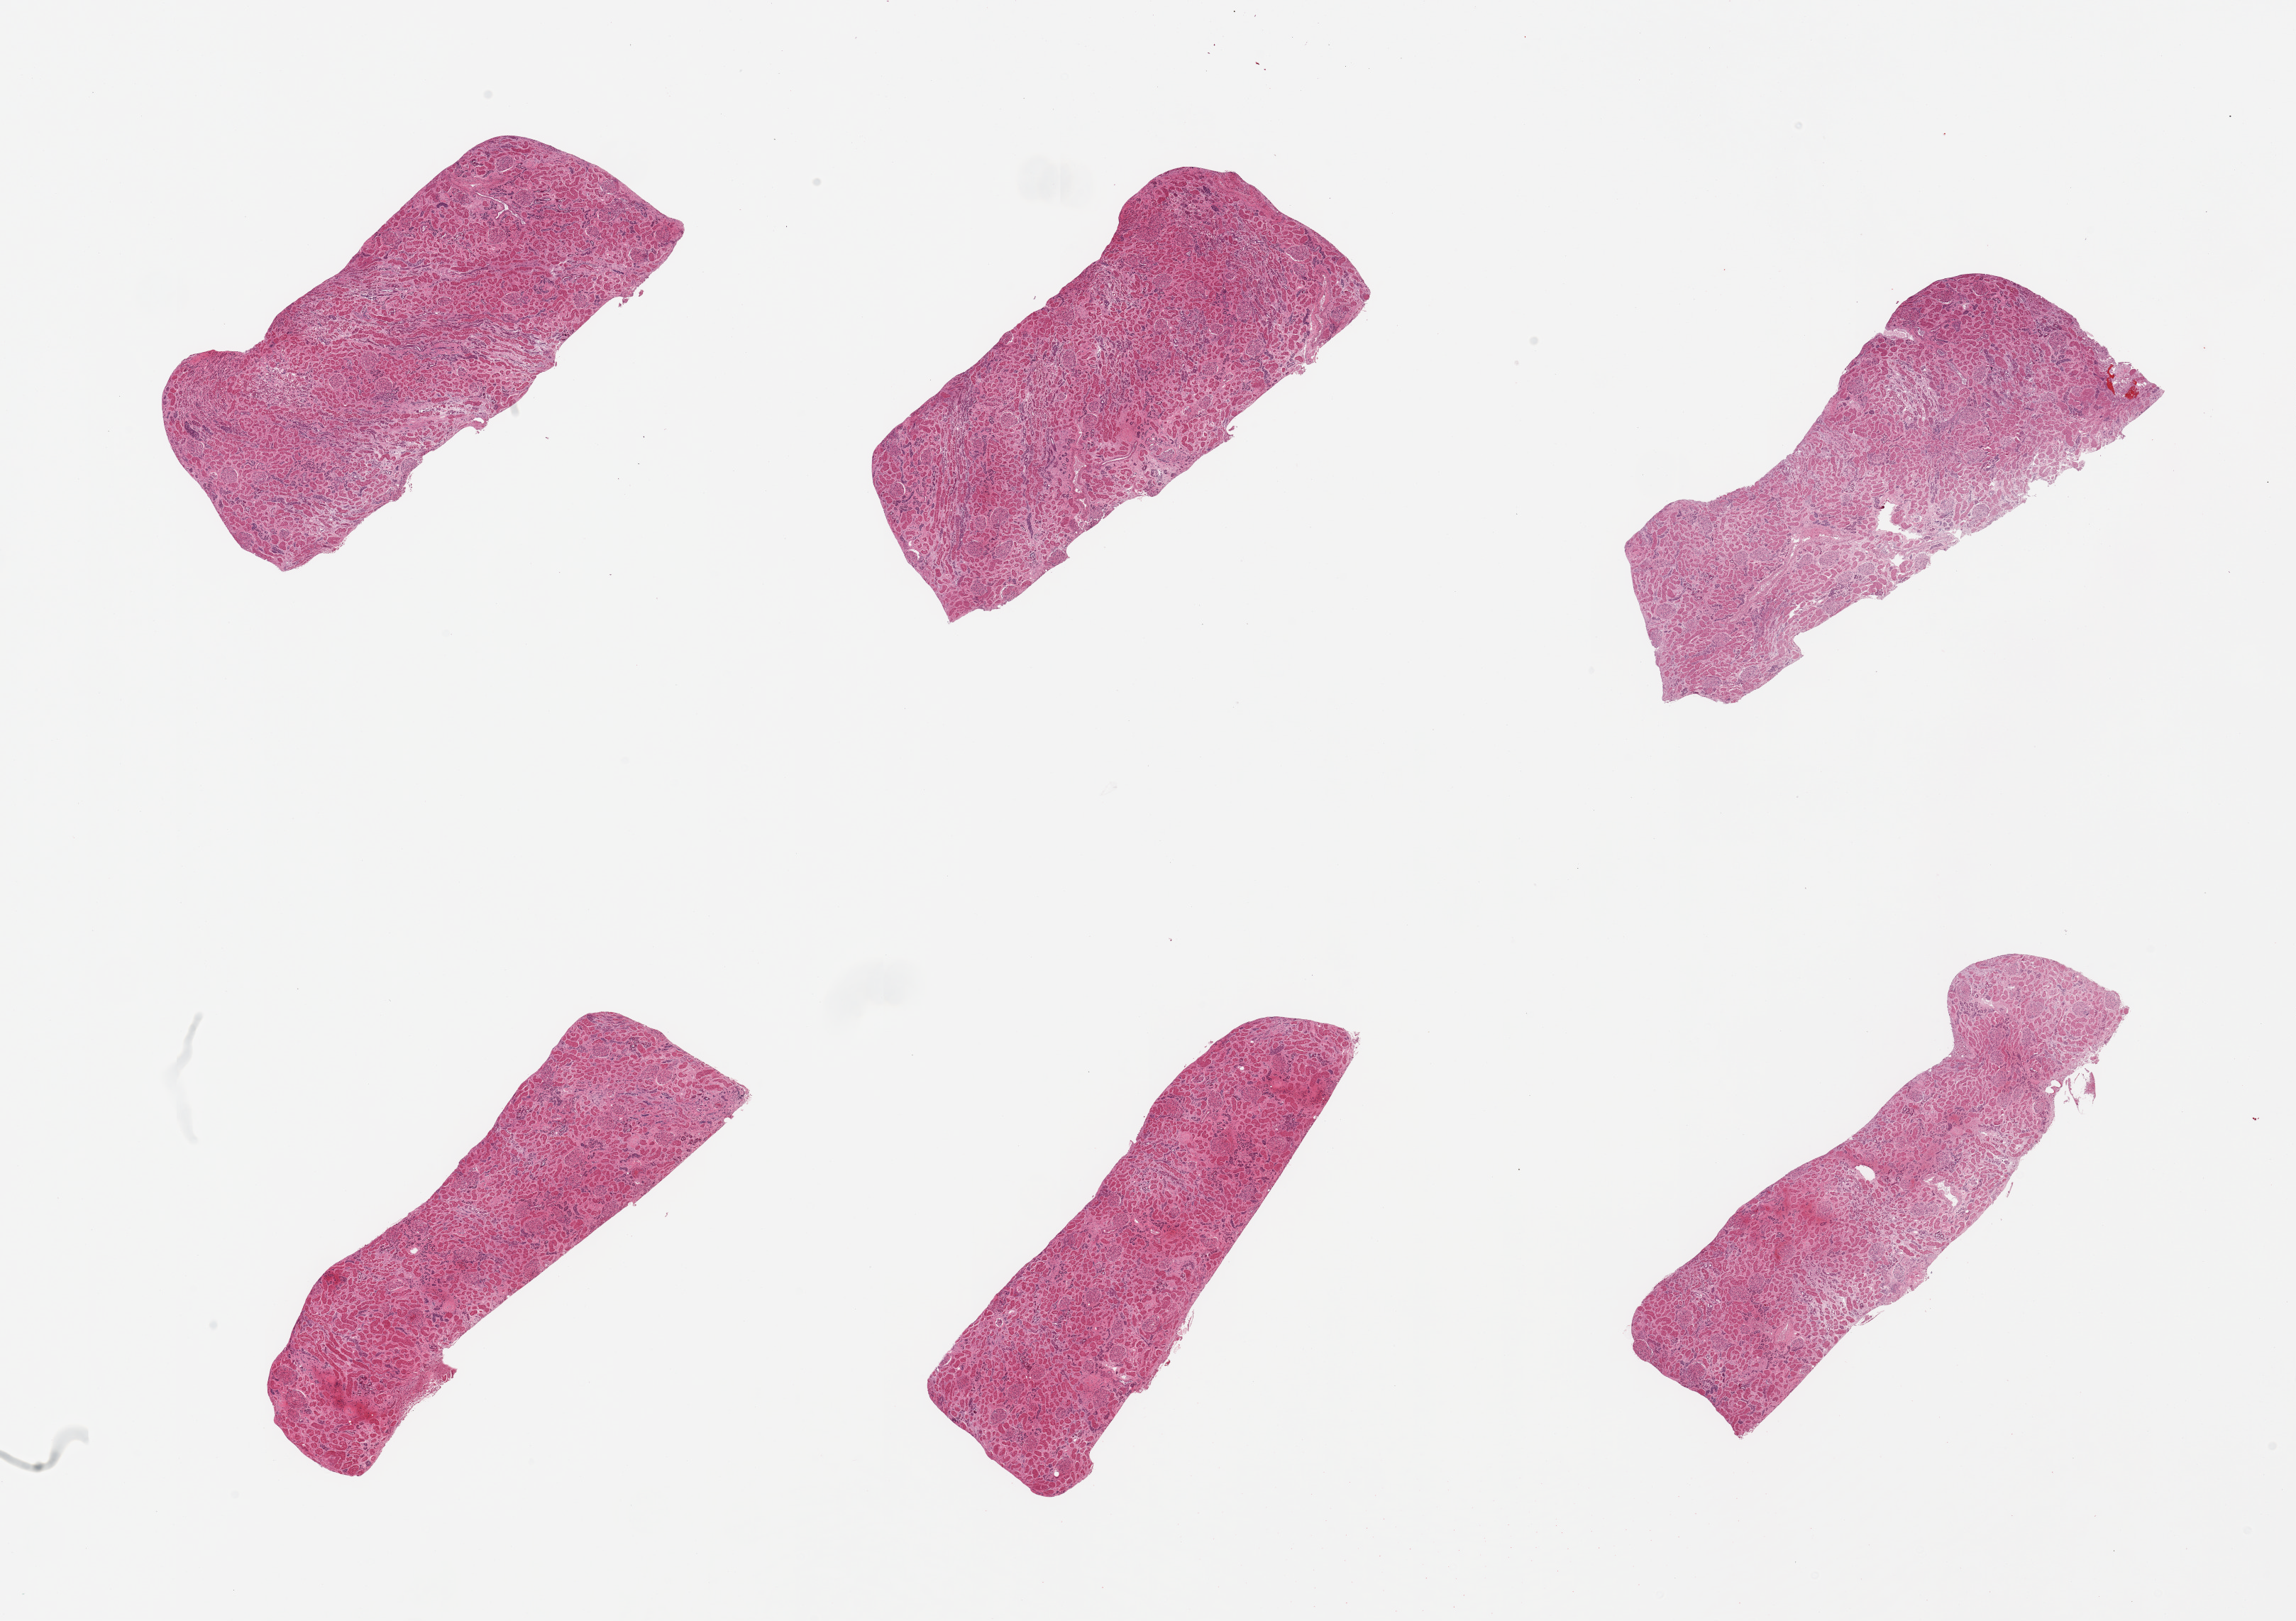
Whole-slide image, hematoxylin and eosin (H&E) stain — low-resolution overview of the scanned area, about 25.6 x 18.1 mm. PAXgene-fixed paraffin-embedded (PFPE) section. Section of renal cortex (target tissue). Tissue donor sample.
- reviewer comment on this tissue sample: 6 pieces, glomeruli present, tubules moderately-markedly autolyzed